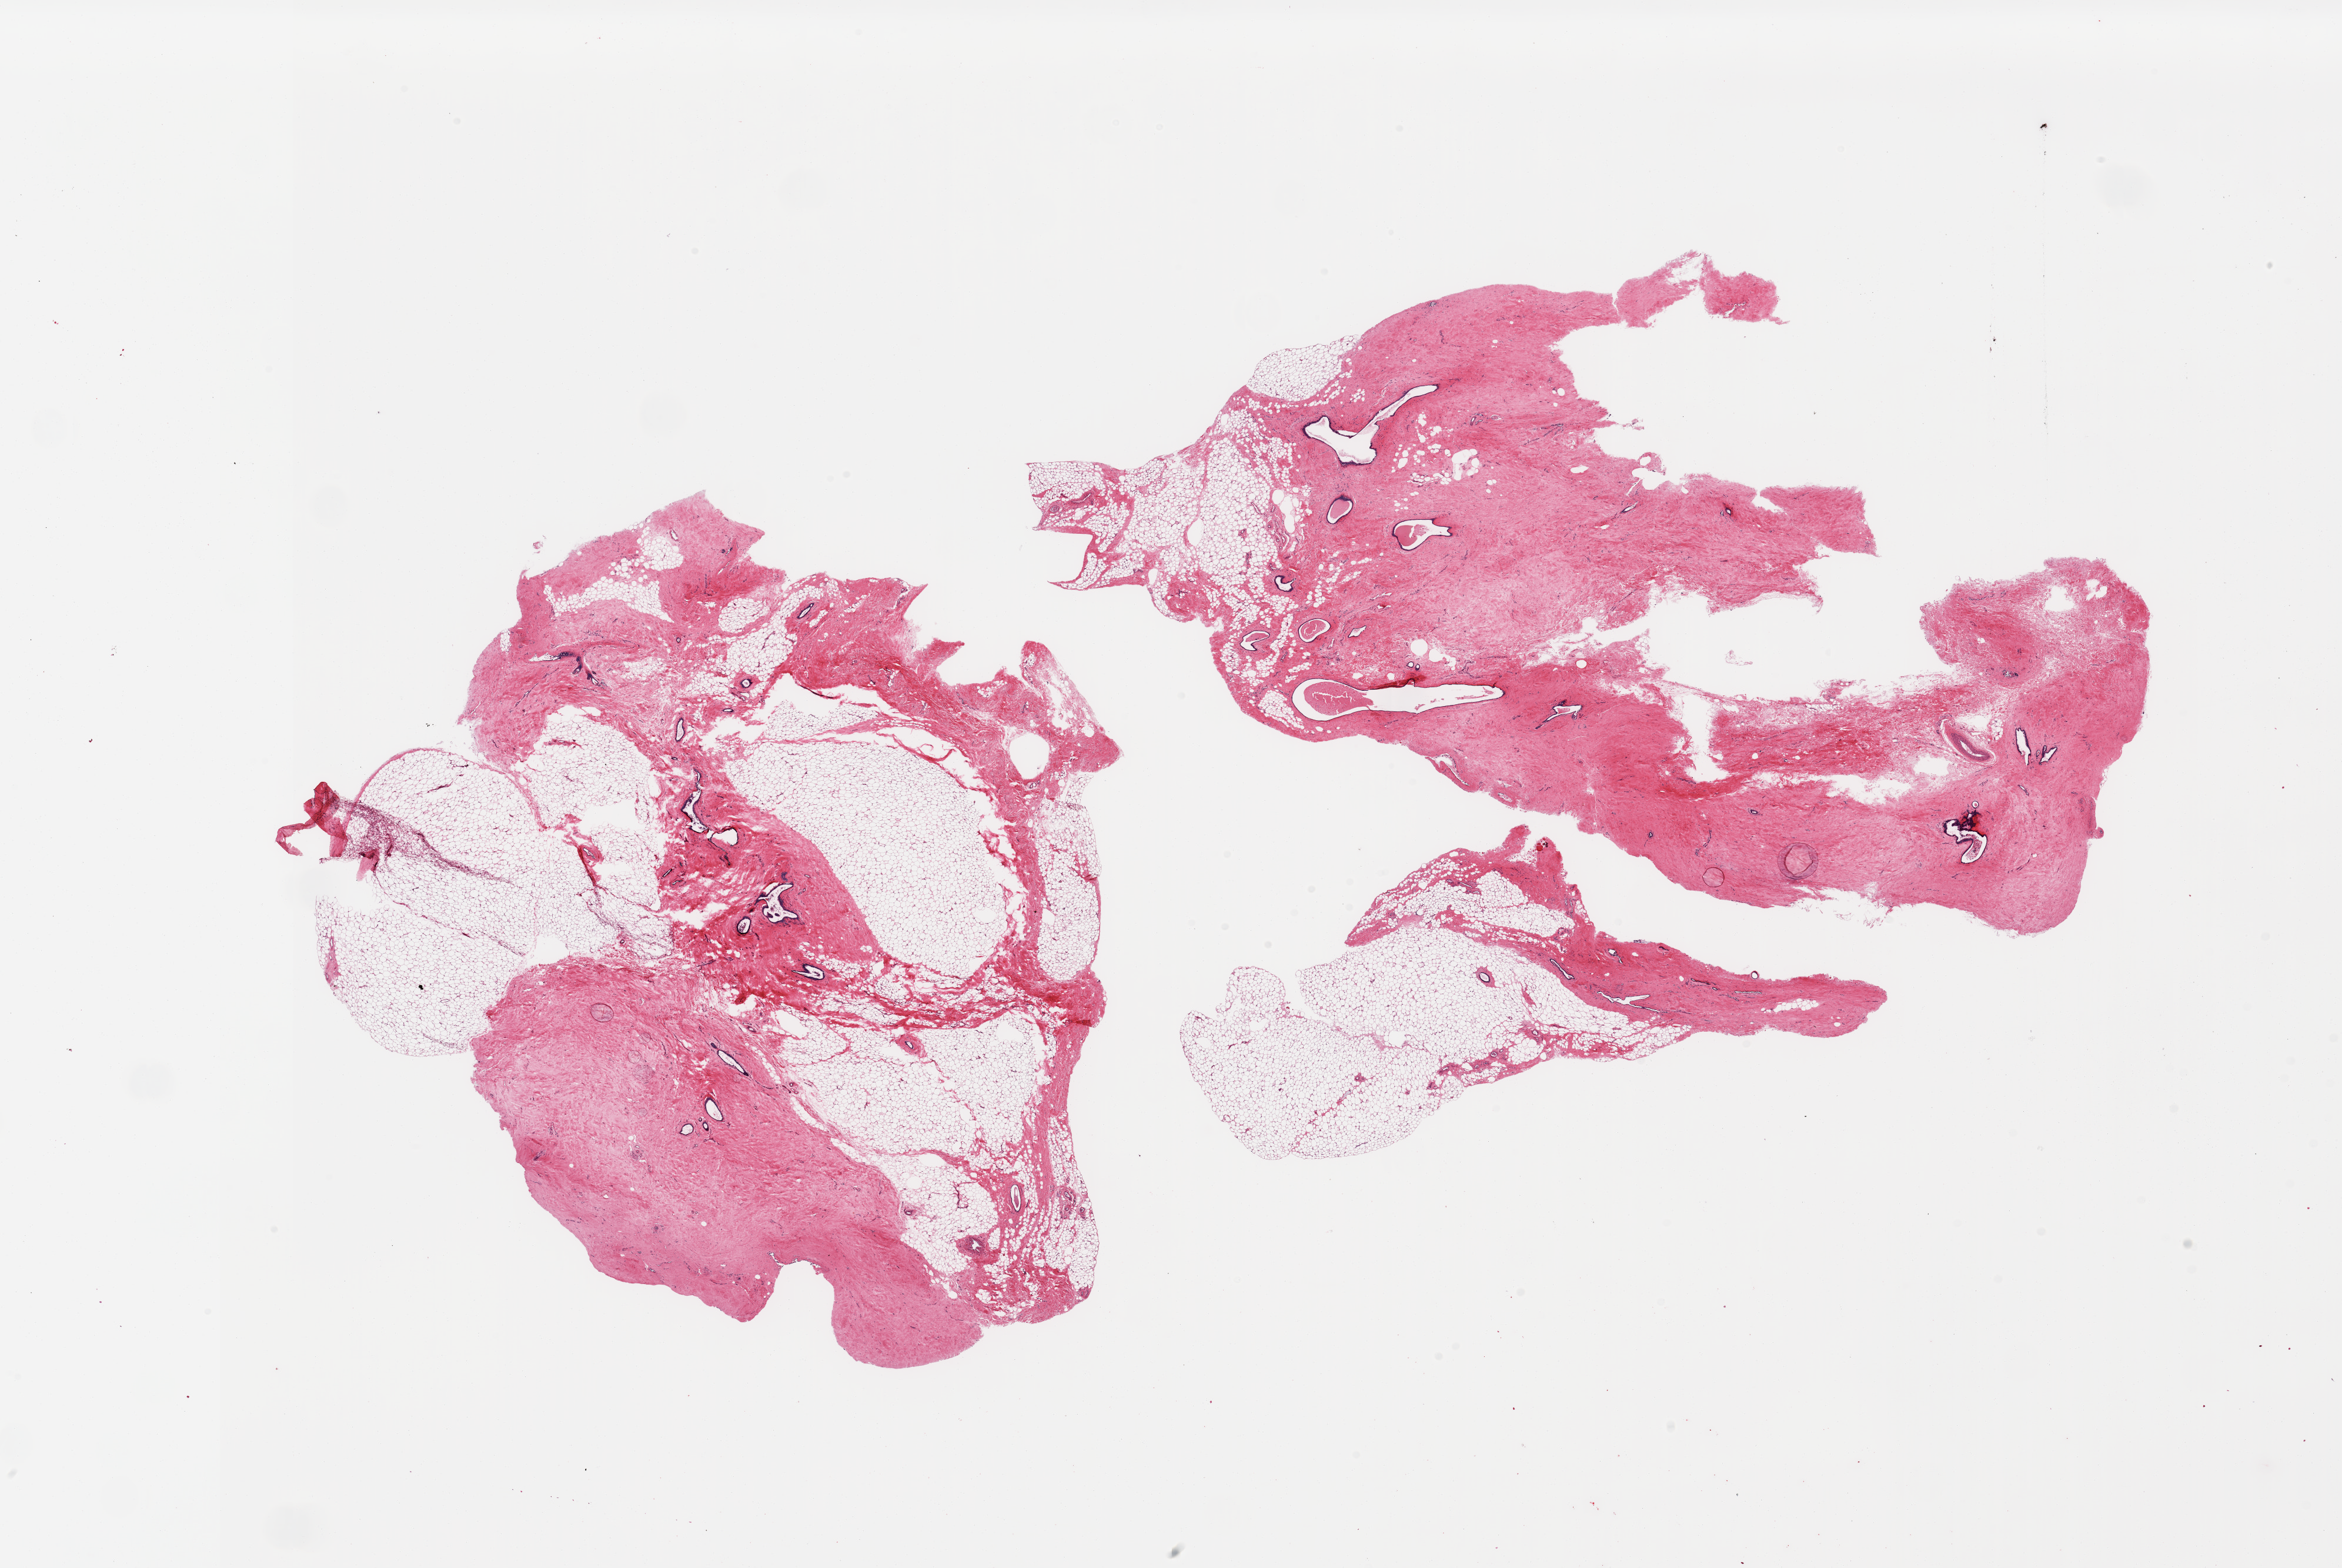
Whole-slide image, hematoxylin and eosin (H&E) stain, shown as a low-resolution overview of the whole scanned area (about 31.5 x 21.1 mm, from a 20x scan), PAXgene-fixed paraffin-embedded (PFPE) section, target tissue: breast, tissue donor sample. Donor: male.
Review note (as recorded): 2 pieces, gynecomastoid stromal, focal ductal hyperplasia.